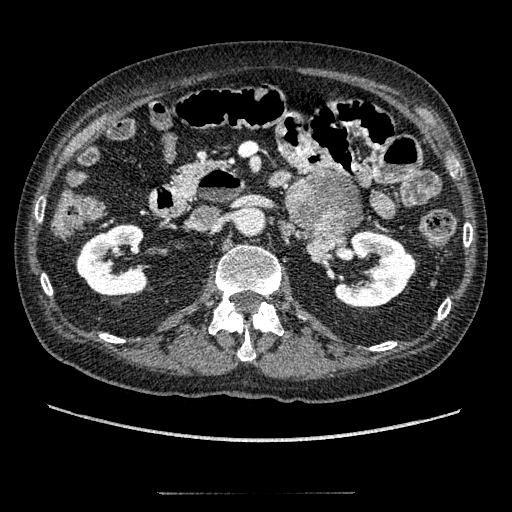
Contrast-enhanced abdominal CT, one axial slice. Slice 95 of 274 in the series (ordered by position). Intravenous contrast given. Soft-tissue window (W 400 / L 40 HU). 512 × 512 image matrix, field of view 381 × 381 mm. Male patient, age 69 years. From the clinical record (not read from this slice): diagnosis: adrenocortical carcinoma; tumour side: left adrenal.
Structures marked on this image (semi-automatically segmented with operator editing):
- mass: bounding box <286,171,360,260> (left, top, right, bottom; pixels)